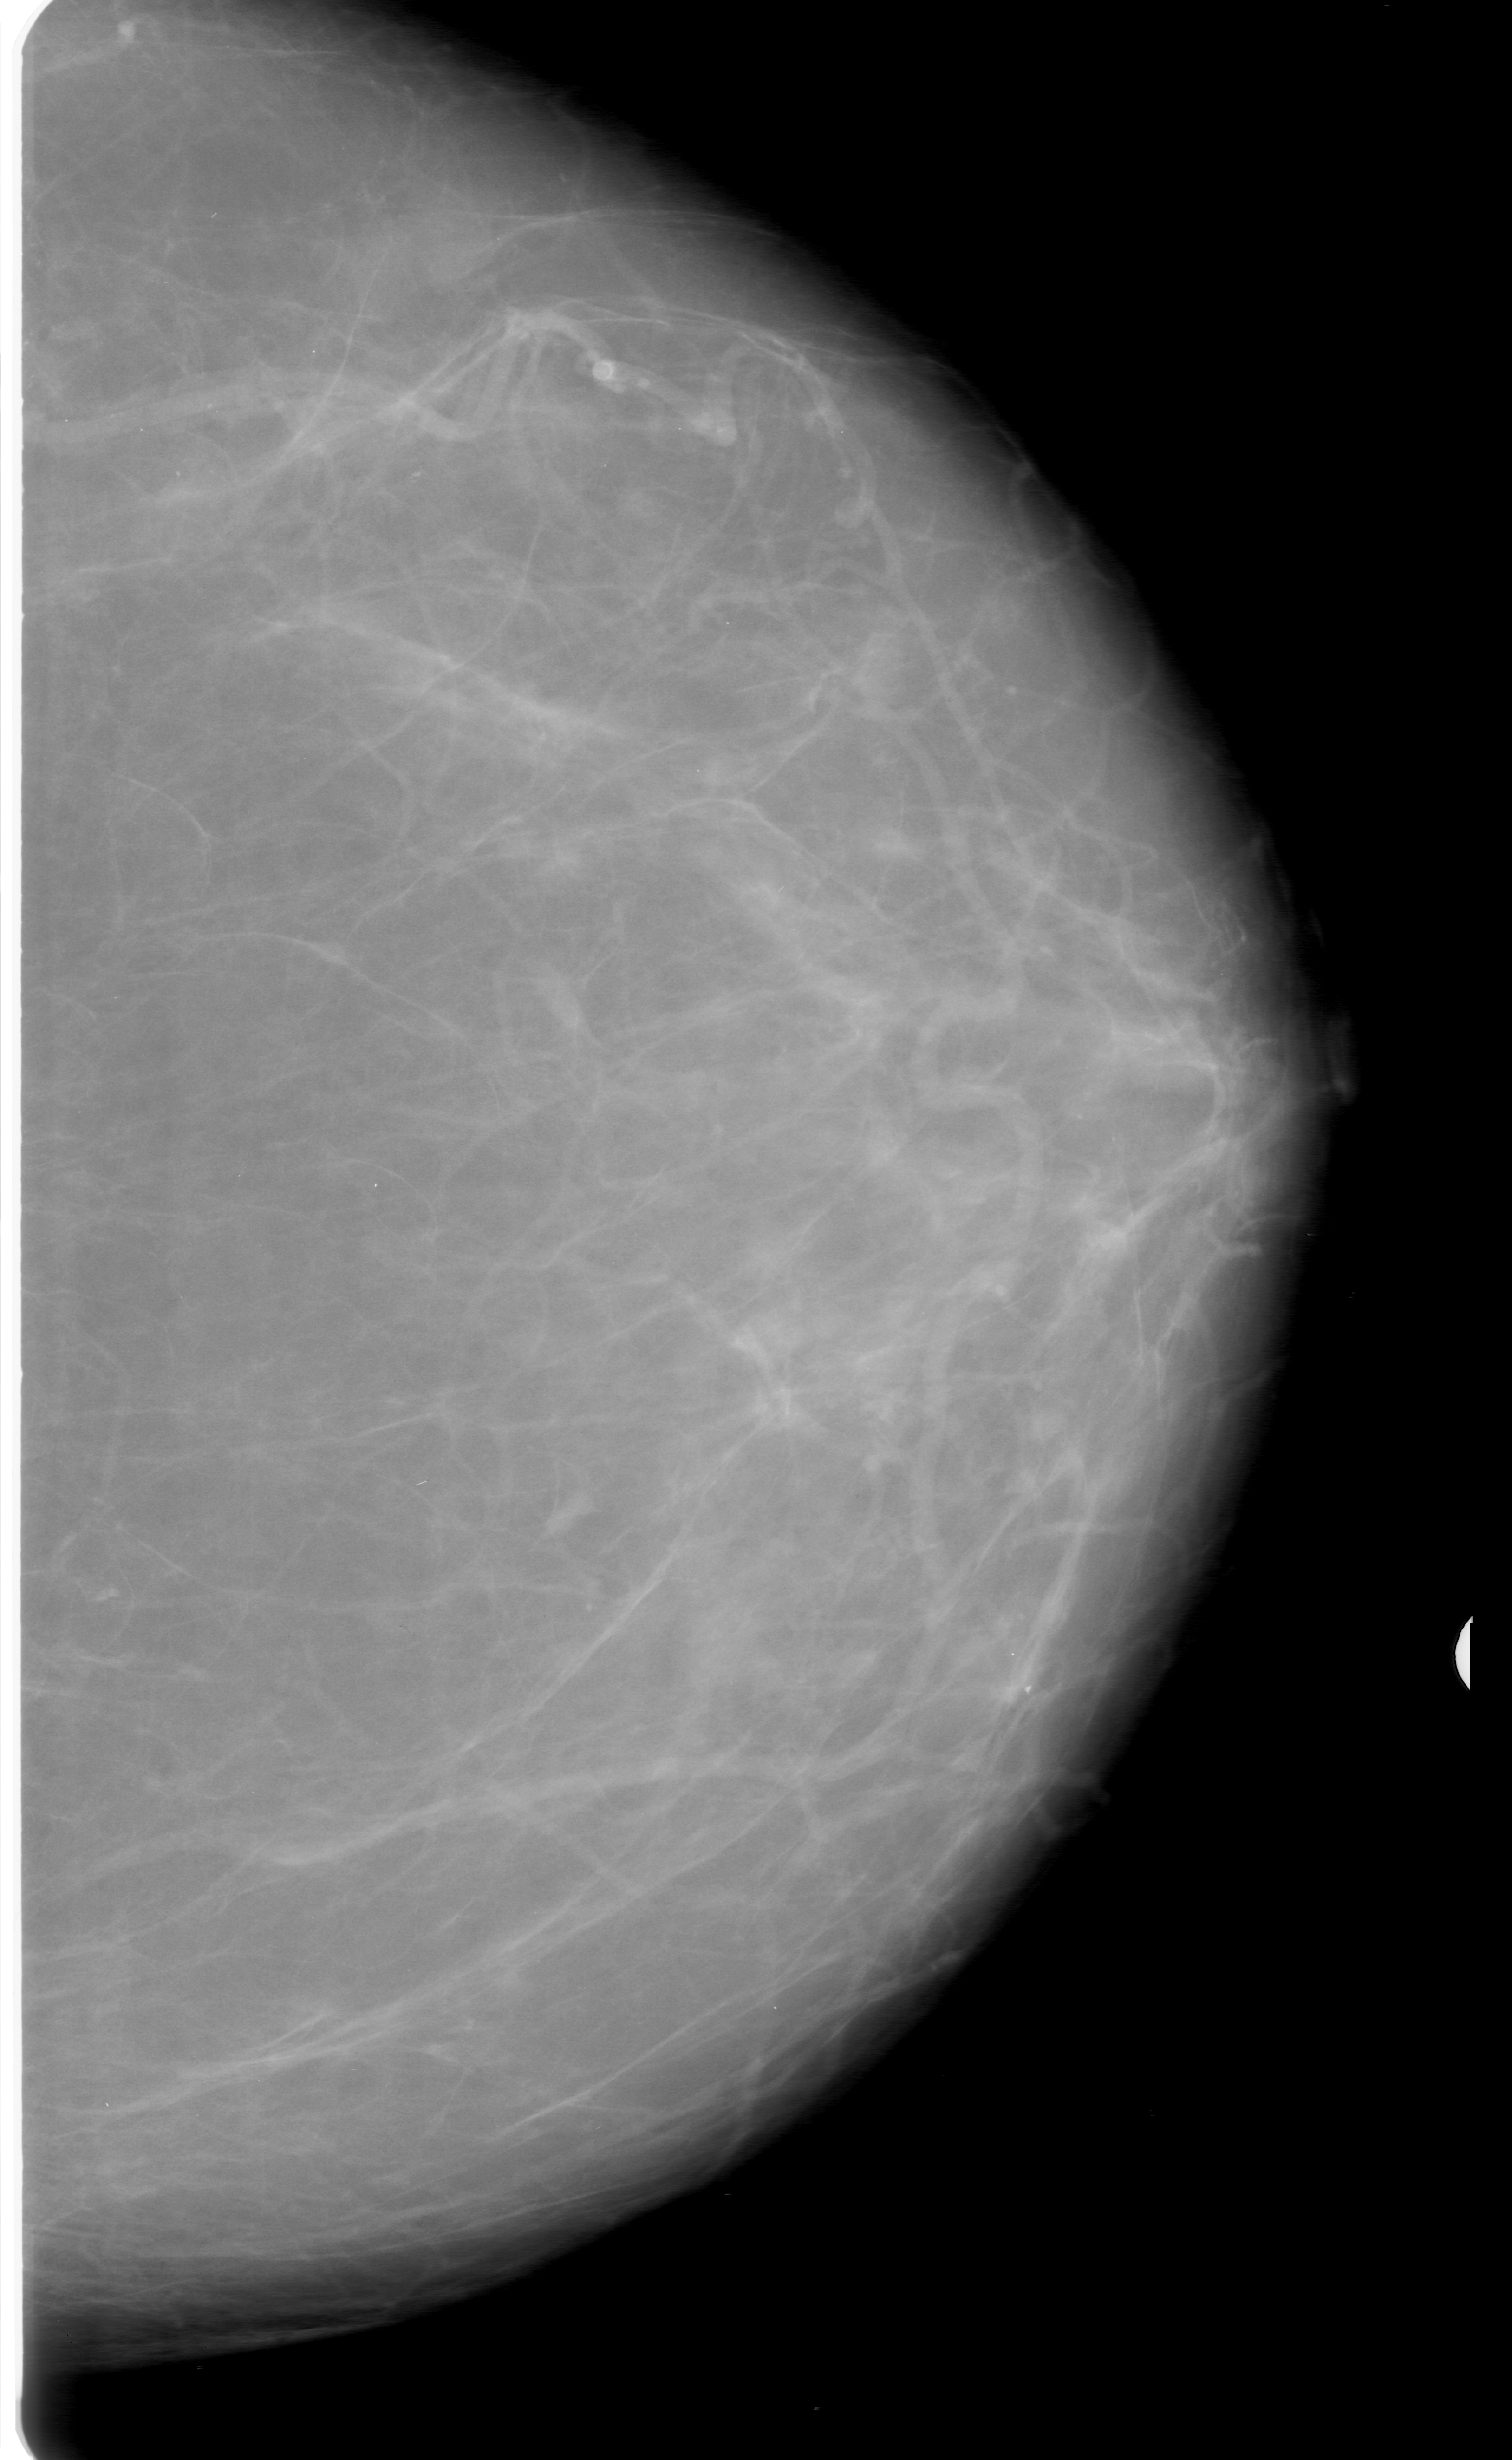
Mammogram (digitized film); left breast; CC view; breast composition: scattered fibroglandular densities (BI-RADS density category 2 of 4); 1512 × 2460 image matrix.
Expert-marked regions of interest on this image (one box per marked abnormality):
- calcifications, morphology amorphous, distribution linear; BI-RADS assessment category 3; subtlety rating 2 on a 1 (subtle) to 5 (obvious) scale; pathology result (as recorded, not read from the image): malignant: box from (x=28, y=133) to (x=176, y=556) px